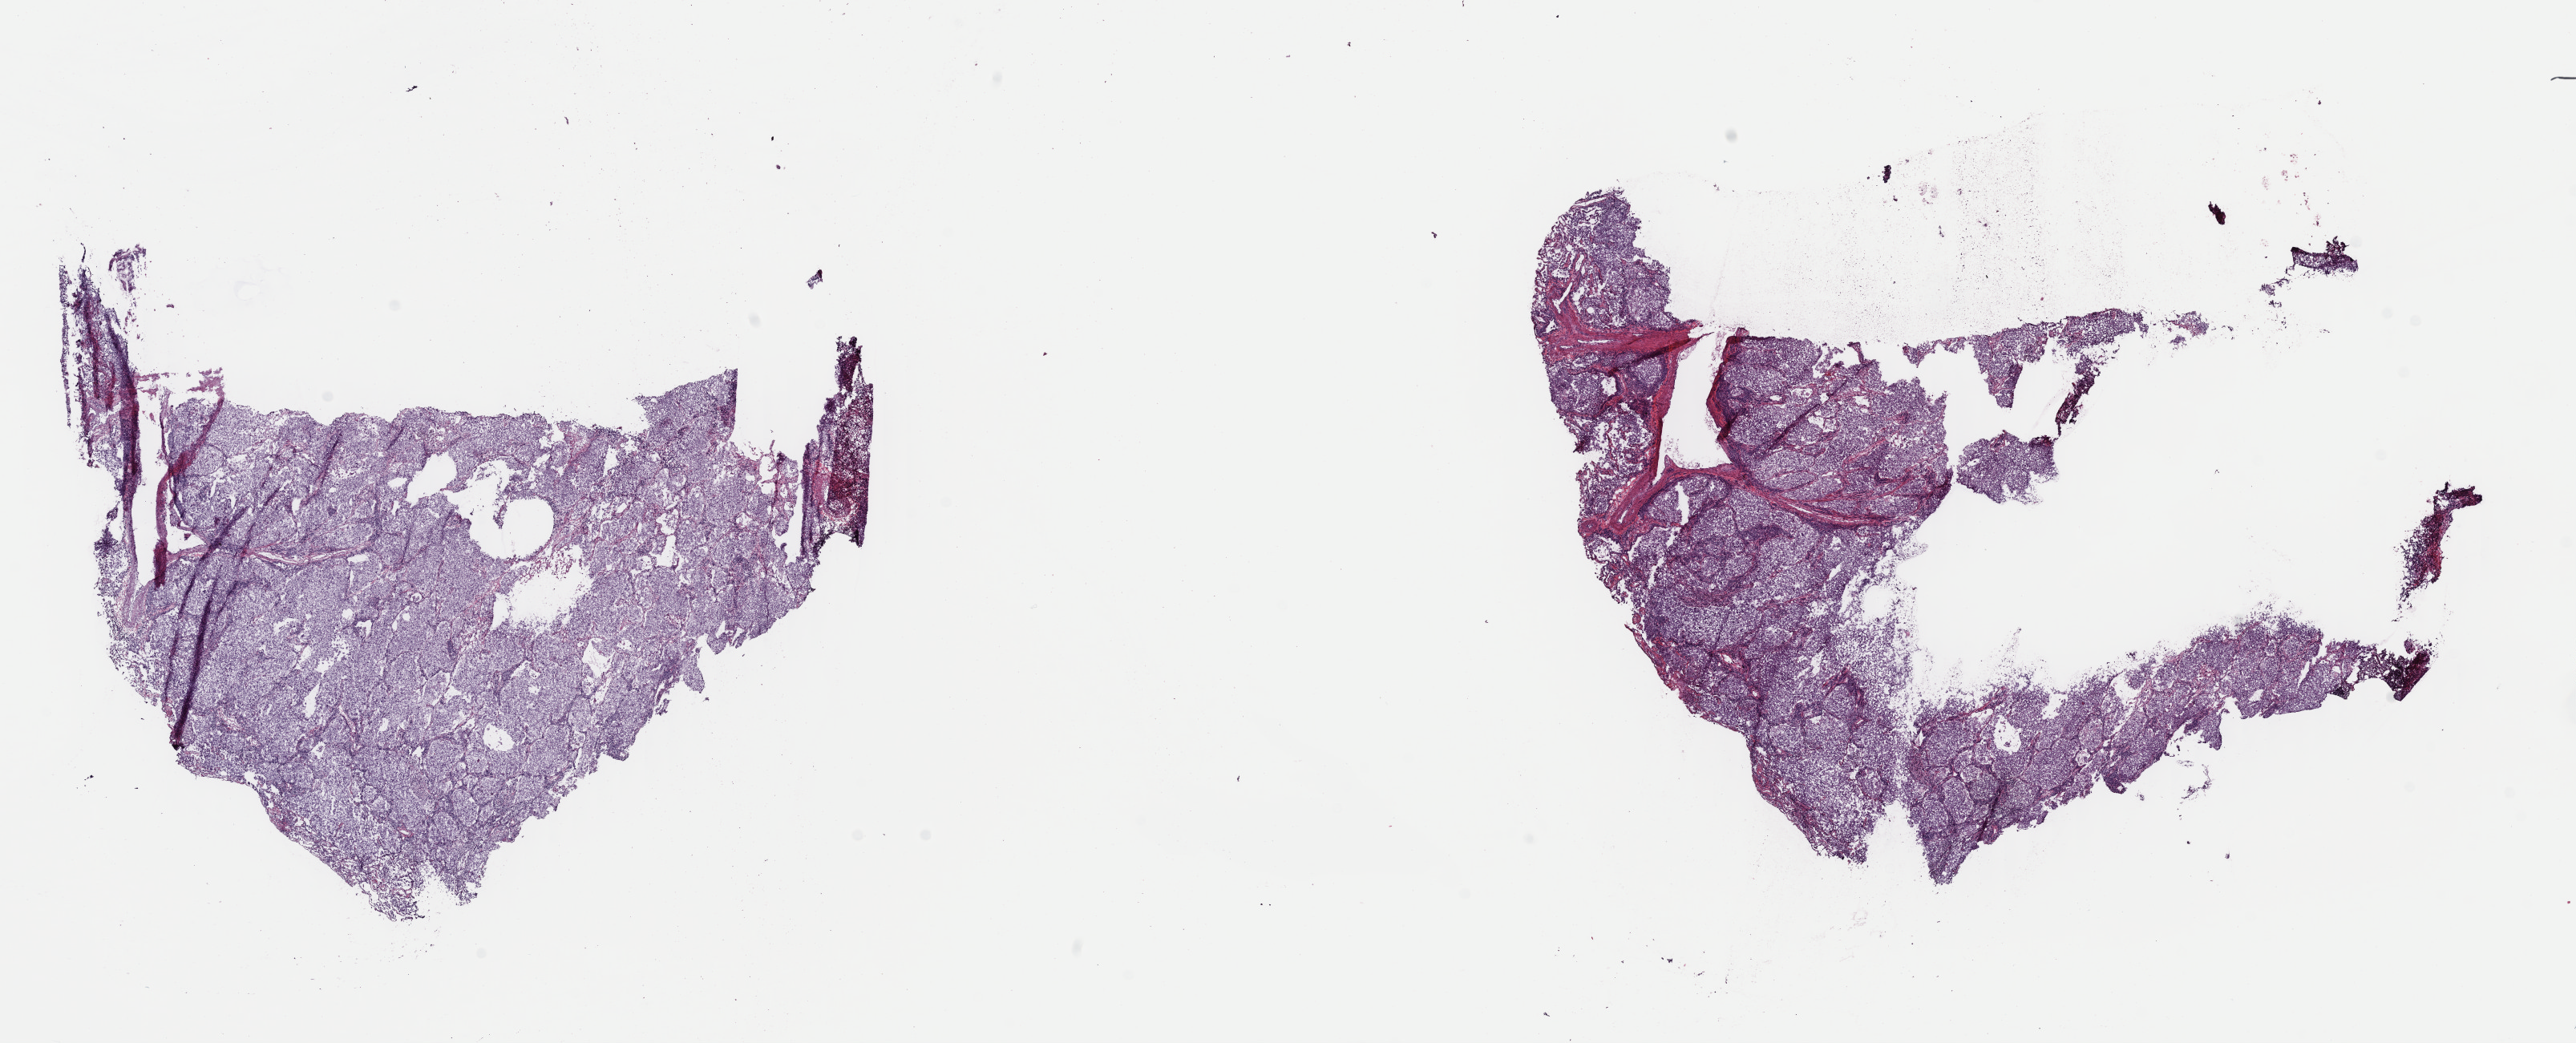
Digitized H&E tissue section (whole slide), shown as a low-resolution overview of the whole scanned area (about 25.3 x 10.3 mm); frozen section from the top of the tissue portion; primary tumour sample from the lung. Female, age 60 years at initial diagnosis. Slide review estimates, as recorded: tumour cells 100%, tumour nuclei 97%, normal cells 0%, stromal cells 0%, necrosis 0%. Inflammatory infiltration, as recorded: lymphocyte infiltration 0%, monocyte infiltration 0%, neutrophil infiltration 0%.
- histologic diagnosis: Adenocarcinoma with mixed subtypes (upper lobe, lung)
- AJCC pathologic stage: IIB (7th edition)